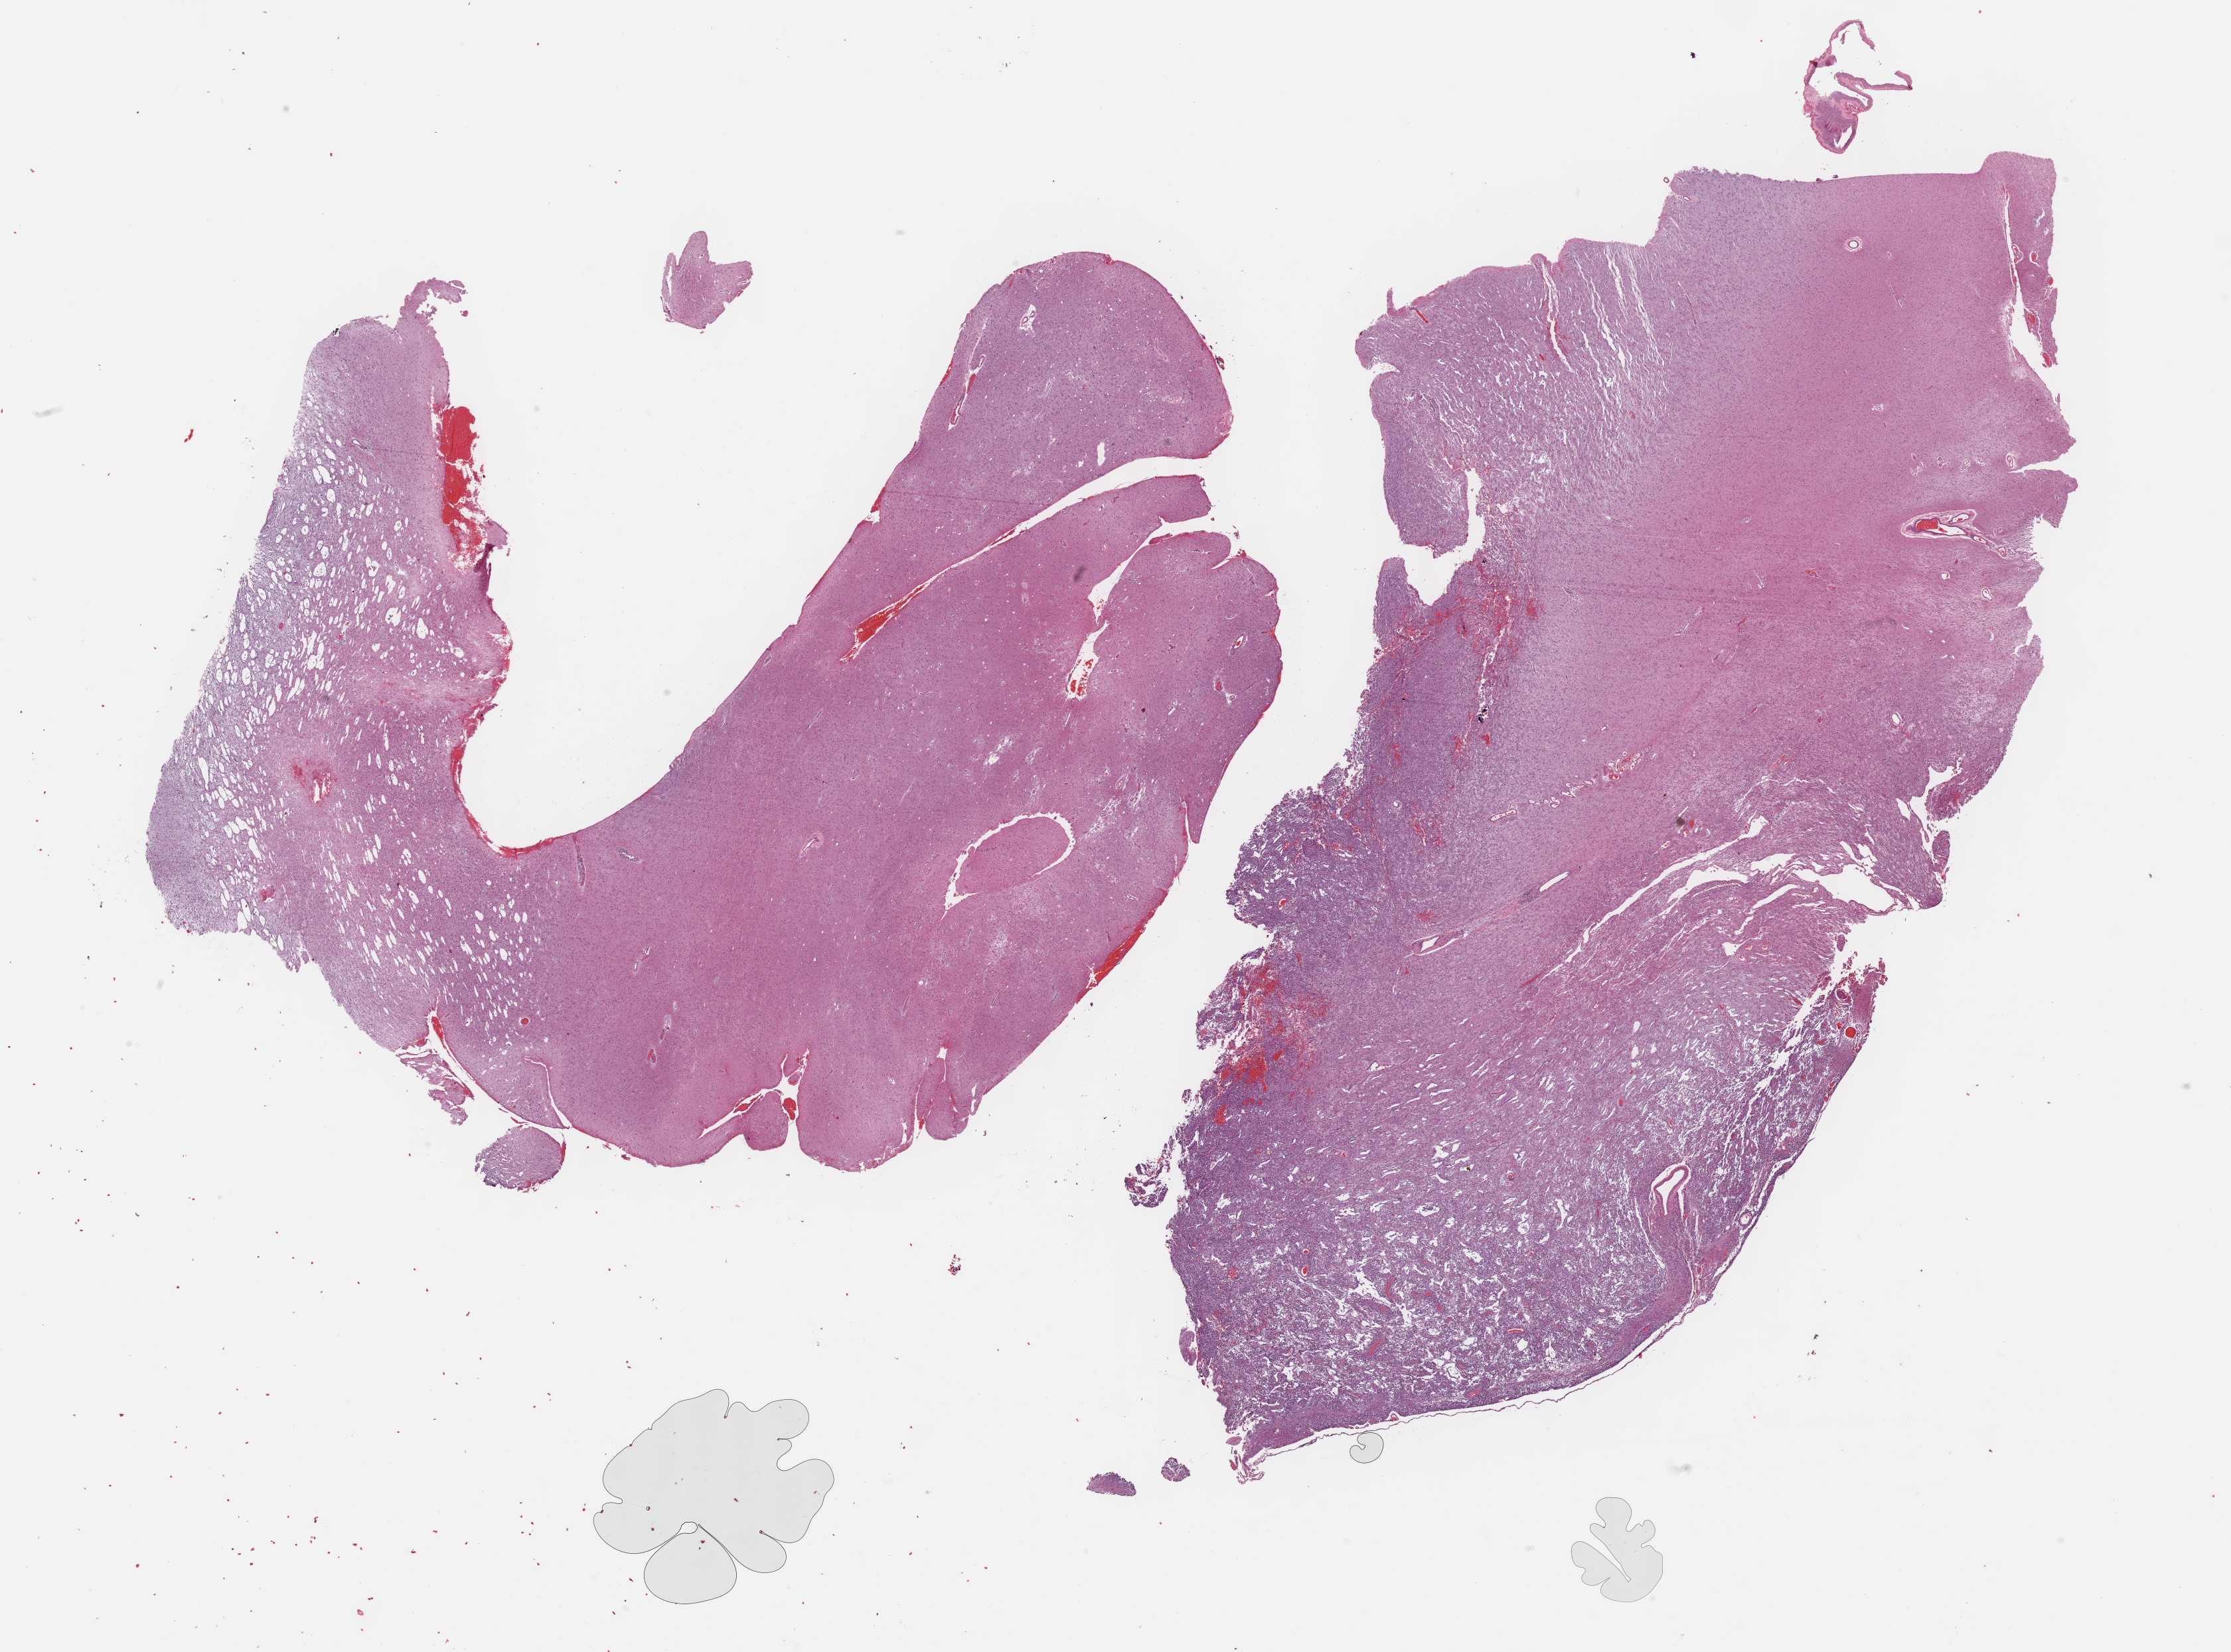
Digitized H&E tissue section (whole slide) — shown as a low-resolution overview of the whole scanned area (about 27.2 x 20.1 mm). Formalin-fixed paraffin-embedded (FFPE) diagnostic section. Brain, primary tumour sample. Male patient; age at initial diagnosis 58 years. Histologic grade: G3 (poorly differentiated).
• laterality: left
• histologic diagnosis: Mixed glioma (cerebrum)